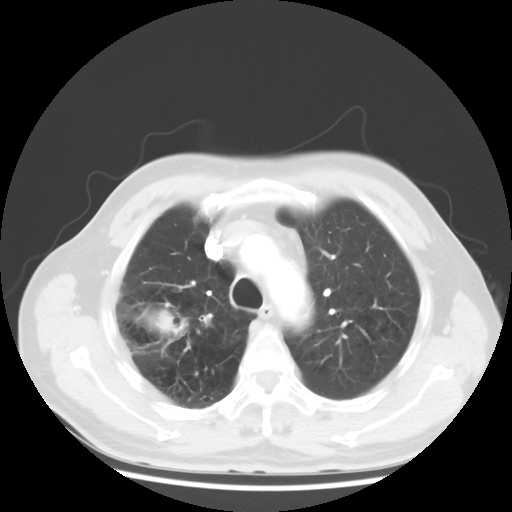
Chest CT, one axial slice. Position 38 of 50 along the scan axis. Reconstruction kernel STANDARD. Lung window (W 1500 / L -600 HU). 5 mm slice thickness. 512 × 512 image matrix, field of view 360 × 360 mm. Patient: male, 69 years. Case-level facts recorded for this patient, not image findings: clinical TNM (as recorded): T3 N0 M0; histopathological grade: G3.
Structures marked on this image (bounding box drawn by a radiologist):
- lung tumour (recorded histology: adenocarcinoma): bounding box [x1, y1, x2, y2] px = [119, 298, 195, 357]